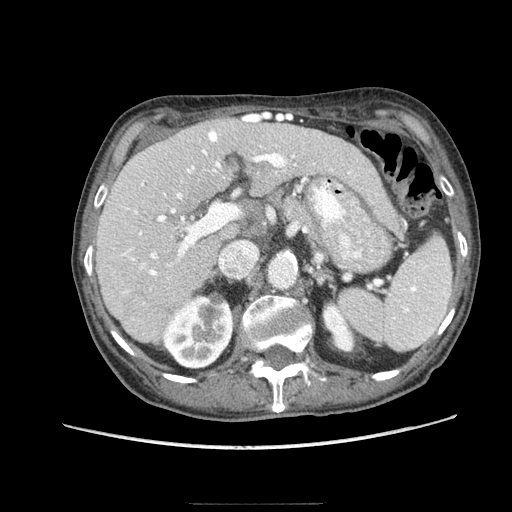
Contrast-enhanced abdominal CT (liver protocol), one axial slice; position 49 of 83 along the scan axis; soft-tissue window (W 400 / L 40 HU); 2.5 mm slice thickness; 512 × 512 image matrix. From the clinical record (not read from this slice): diagnosis: hepatocellular carcinoma (patient treated with transarterial chemoembolisation; whether this scan precedes or follows treatment is not stated here); TNM stage (as recorded): Stage-I; Child-Pugh class: A; tumour differentiation: moderately differentiated; tumour nodularity: uninodular.
Structures marked on this image (semi-automatically segmented with operator editing):
- liver parenchyma outside the tumour (the mass and vessels are separate outlines, so this box may not span the whole liver): box from (x=96, y=116) to (x=364, y=343) px
- liver vessels: (x=122, y=115)–(x=333, y=293)